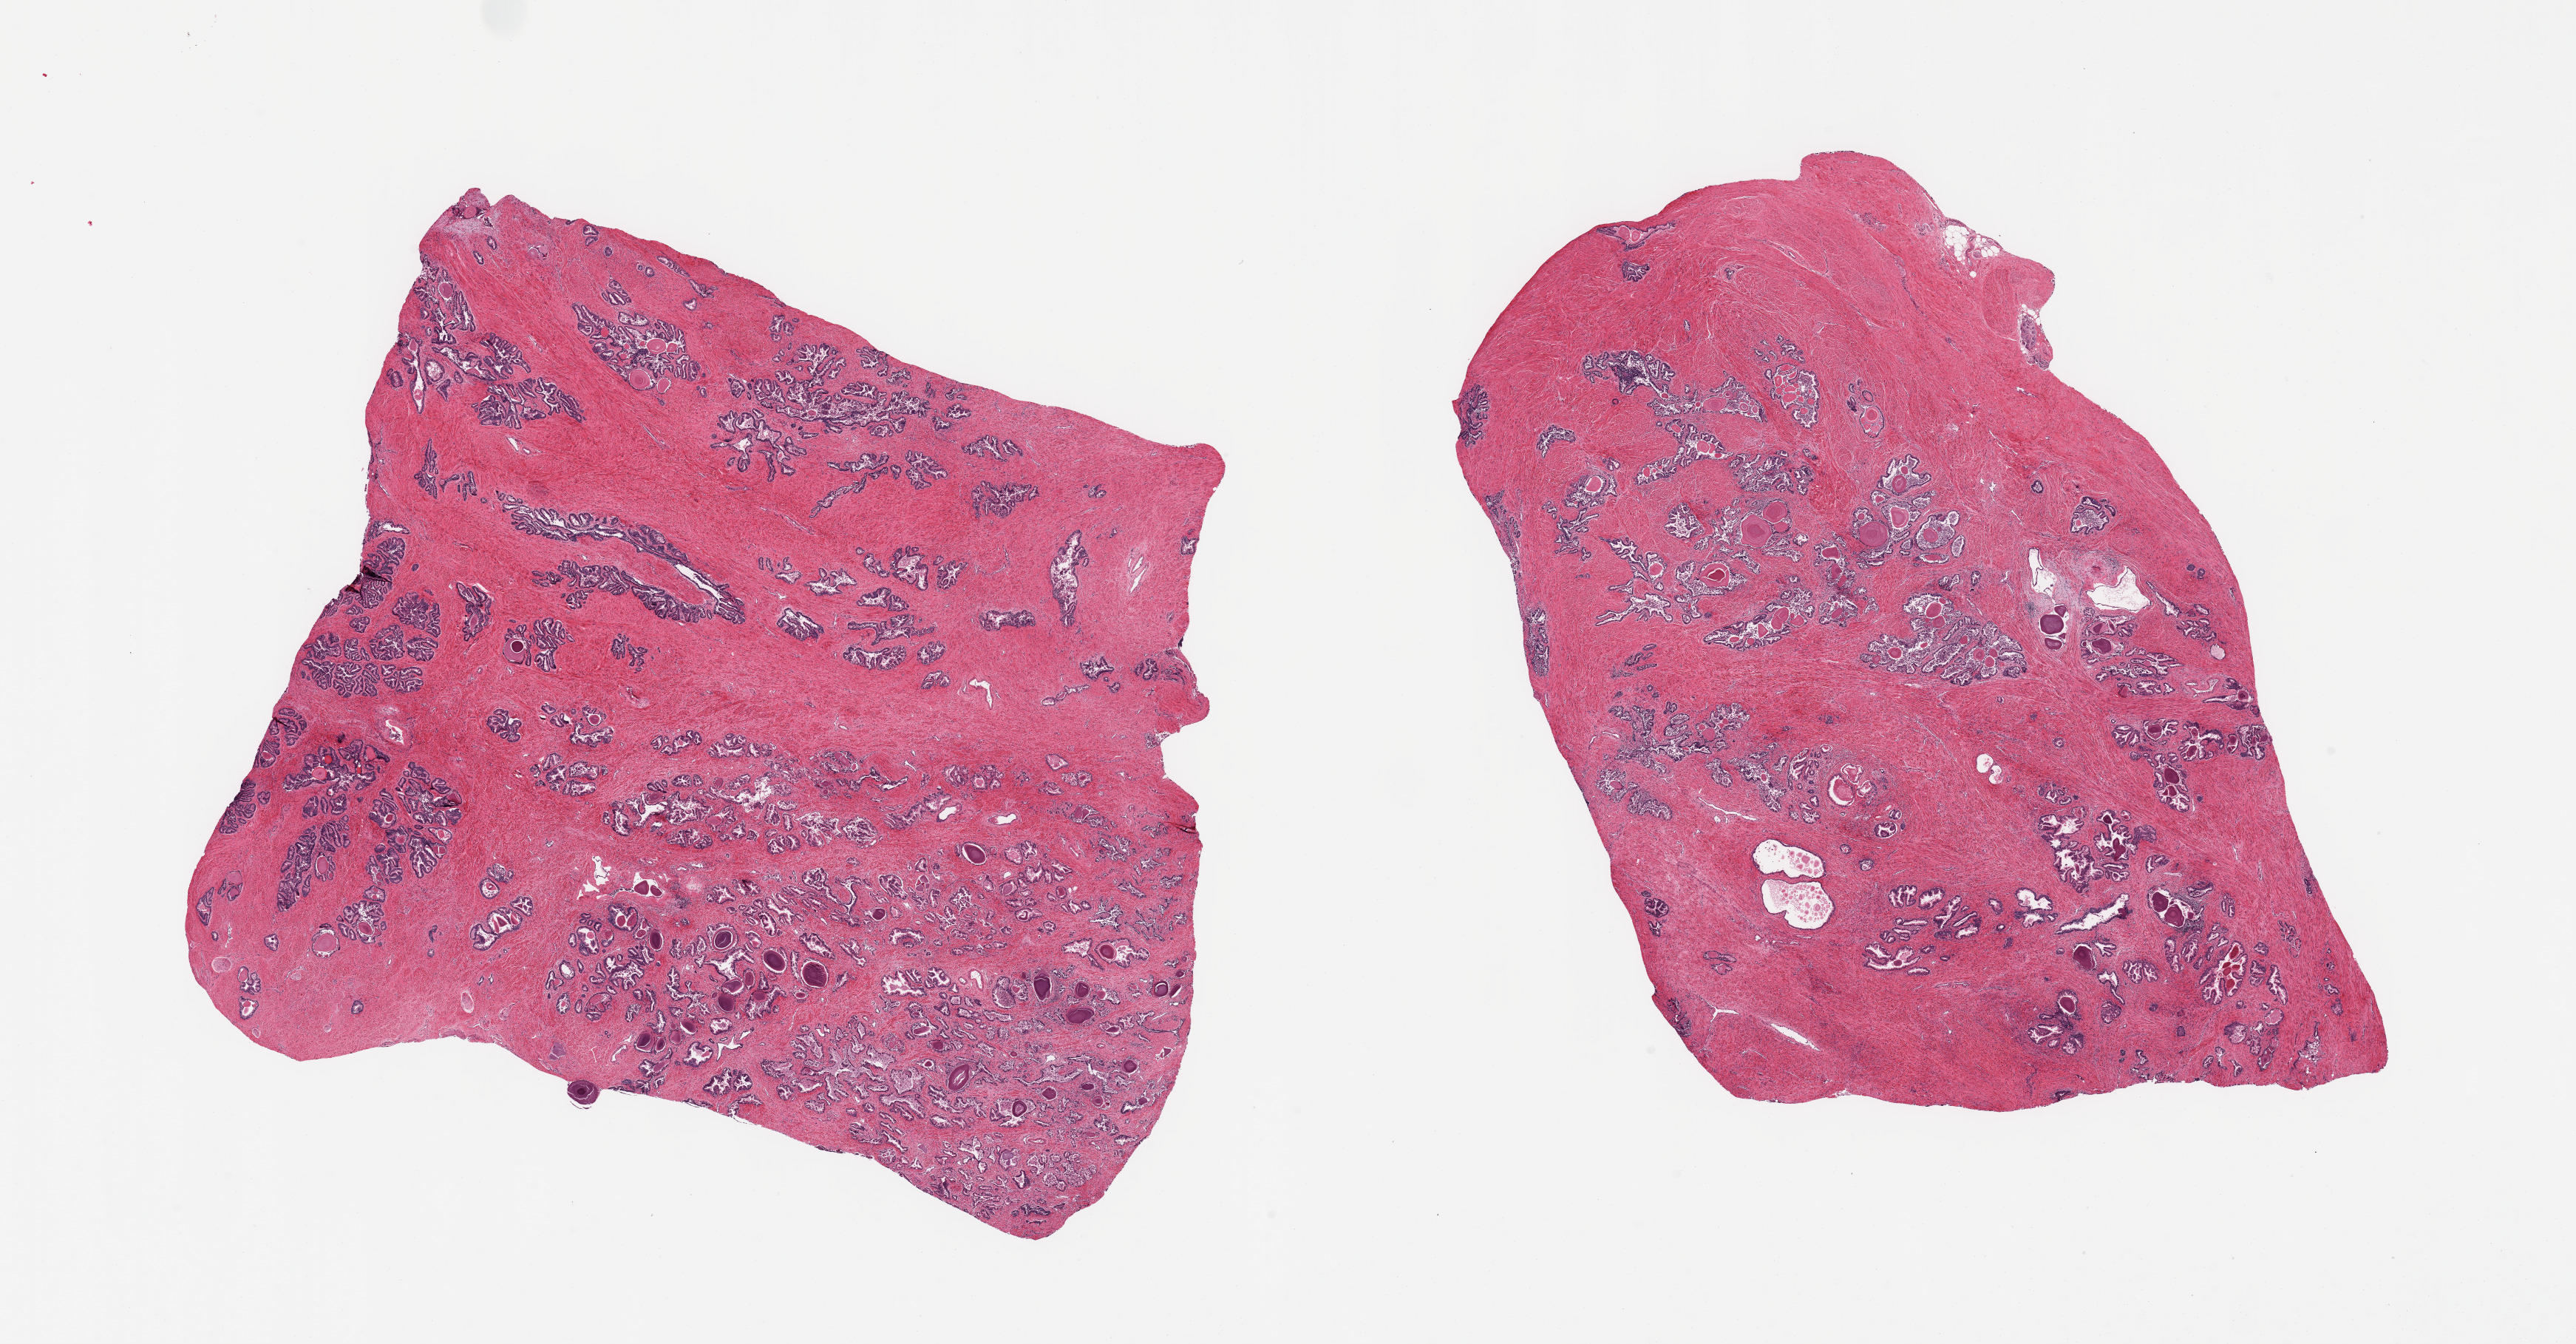
Digitized H&E-stained section — a low-resolution overview of the entire scanned area, about 27.6 x 14.4 mm (slide scanned at 20x); PAXgene-fixed paraffin-embedded (PFPE) section; sampled site (target tissue): prostate; tissue donor sample. Donor: male.
Reviewer comment on this tissue sample: 2 pieces; glands moderately autolyzed; stroma well preserved.